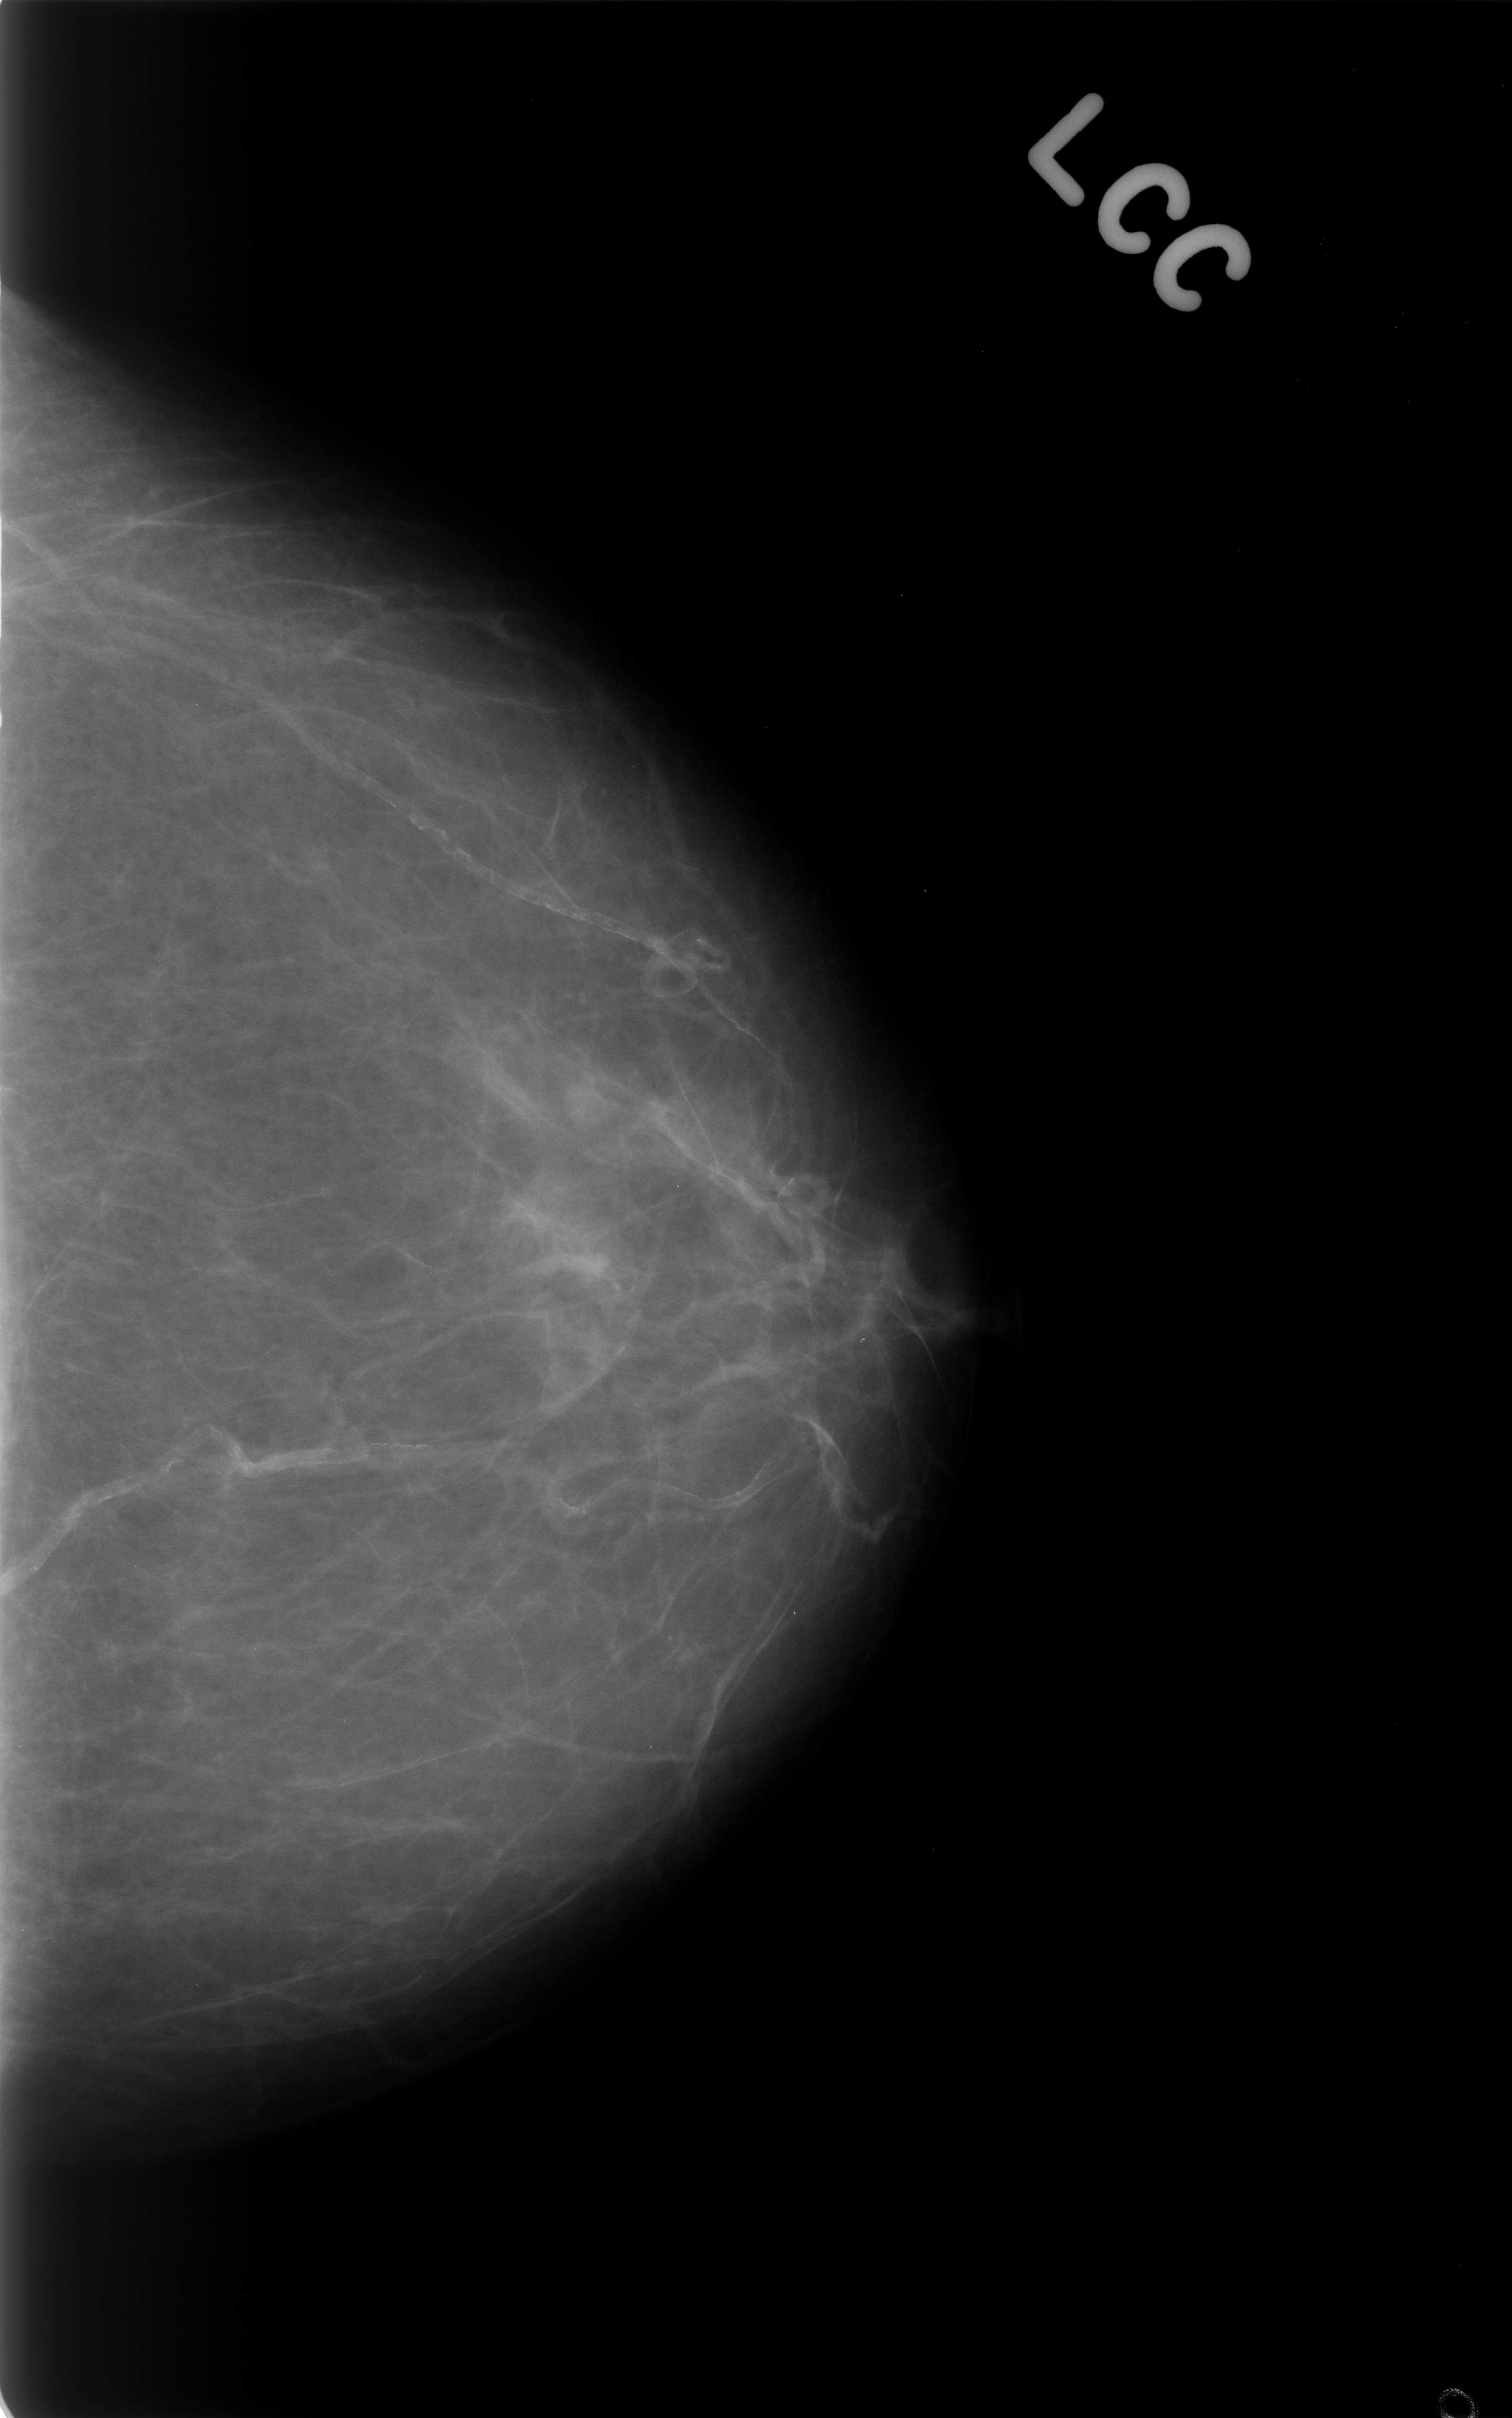
Scanned film-screen mammogram, left breast, craniocaudal (CC) view, BI-RADS breast density category 1 (scale 1–4).
Abnormality record for this image: mass, shape lobulated, margins circumscribed; BI-RADS assessment category 3; subtlety rating 4 on a 1 (subtle) to 5 (obvious) scale; pathology (as recorded): benign.